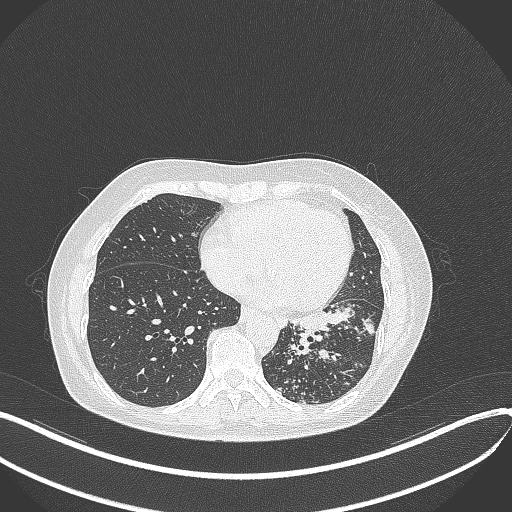
Chest CT, one axial slice; slice 146 of 429 in the series (ordered by position); 100 kVp; lung window (W 1500 / L -600 HU); 512 × 512 image matrix. Female patient, age 63 years. Case-level facts recorded for this patient, not image findings: clinical TNM (as recorded): T1b N0 M0.
Structures marked on this image (rectangle marked by the reading radiologist):
- lung tumour (recorded histology: adenocarcinoma): box from (x=287, y=300) to (x=377, y=335) px